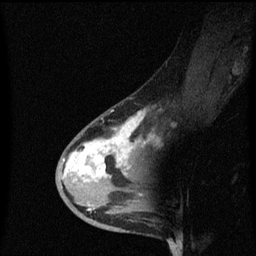
Breast MRI (dynamic contrast-enhanced), one sagittal slice. Slice 32 of 60 in the series (ordered by position). Dynamic contrast-enhanced series, image 2 of 3 at this slice position (ordered by acquisition). 1.5 T. TE 4.2 ms, TR 8.4 ms. 2 mm slice thickness. 256 × 256 image matrix. Female patient, age 38 years. Case-level facts recorded for this patient, not image findings: setting: breast cancer imaged before/during neoadjuvant chemotherapy; receptor status: HR-positive, HER2-negative.
Structures marked on this image (semi-automatically segmented with operator editing):
- analysis volume of interest (the breast-tissue region the enhancement analysis was run in; not a lesion): bounding box (x1, y1, x2, y2) in pixels: (56, 104, 149, 205)
- tumour enhancement mask (voxels above the 70 % enhancement threshold inside the analysis volume of interest): (64, 112, 145, 177)